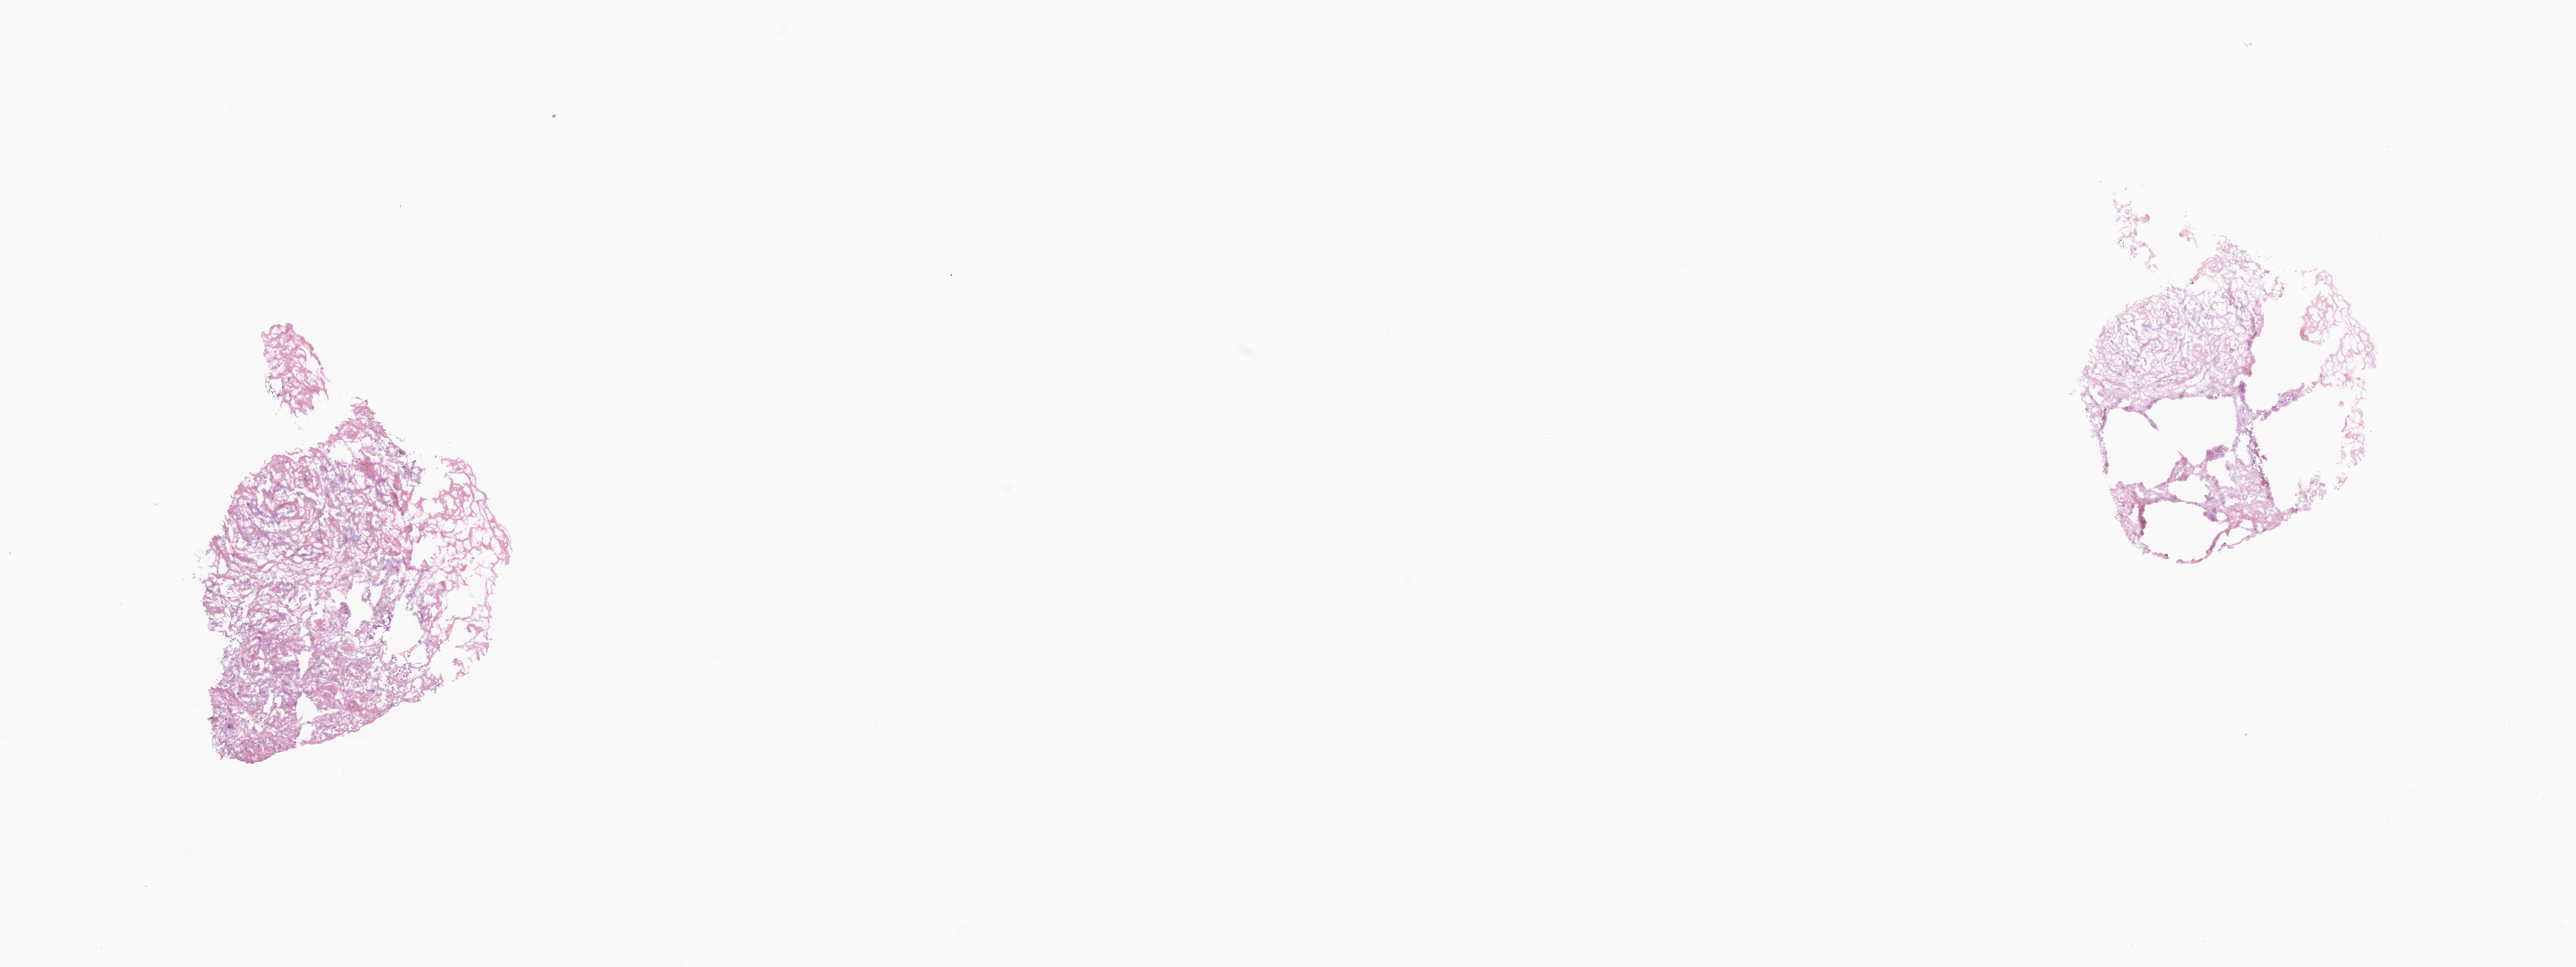
Whole-slide image, hematoxylin and eosin (H&E) stain — shown as a low-resolution overview of the whole scanned area (about 24.0 x 9.0 mm). Frozen section (tissue freezing medium). Specimen: primary tumor. Anatomic site: breast. Female, age 69 years at initial diagnosis. Pathologist review of this section (percent, as recorded): tumor cells 85%, tumor nuclei 70%, stromal cells 0%, necrosis 0%, normal cells 15%. Infiltration values recorded for this section: lymphocyte infiltration 0%, monocyte infiltration 0%, neutrophil infiltration 0%.
Diagnosis: Infiltrating duct carcinoma, NOS. Section: top of the tissue portion.